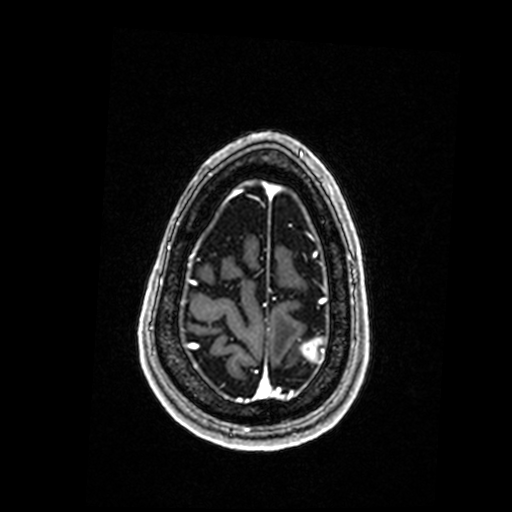
Brain MRI from a brain-tumour surgery series, one axial slice; position 37 of 192 along the scan axis; T1-weighted post-contrast; 0.98 mm slice thickness; 512 × 512 image matrix, field of view 250 × 250 mm. From the clinical record (not read from this slice): histopathology: Metastastic Carcinoma, Poorly Differentiated; tumour location: Left Parietal.
Structures marked on this image (expert manual segmentation):
- tumour: bounding box (x1, y1, x2, y2) in pixels: (302, 339, 325, 363)